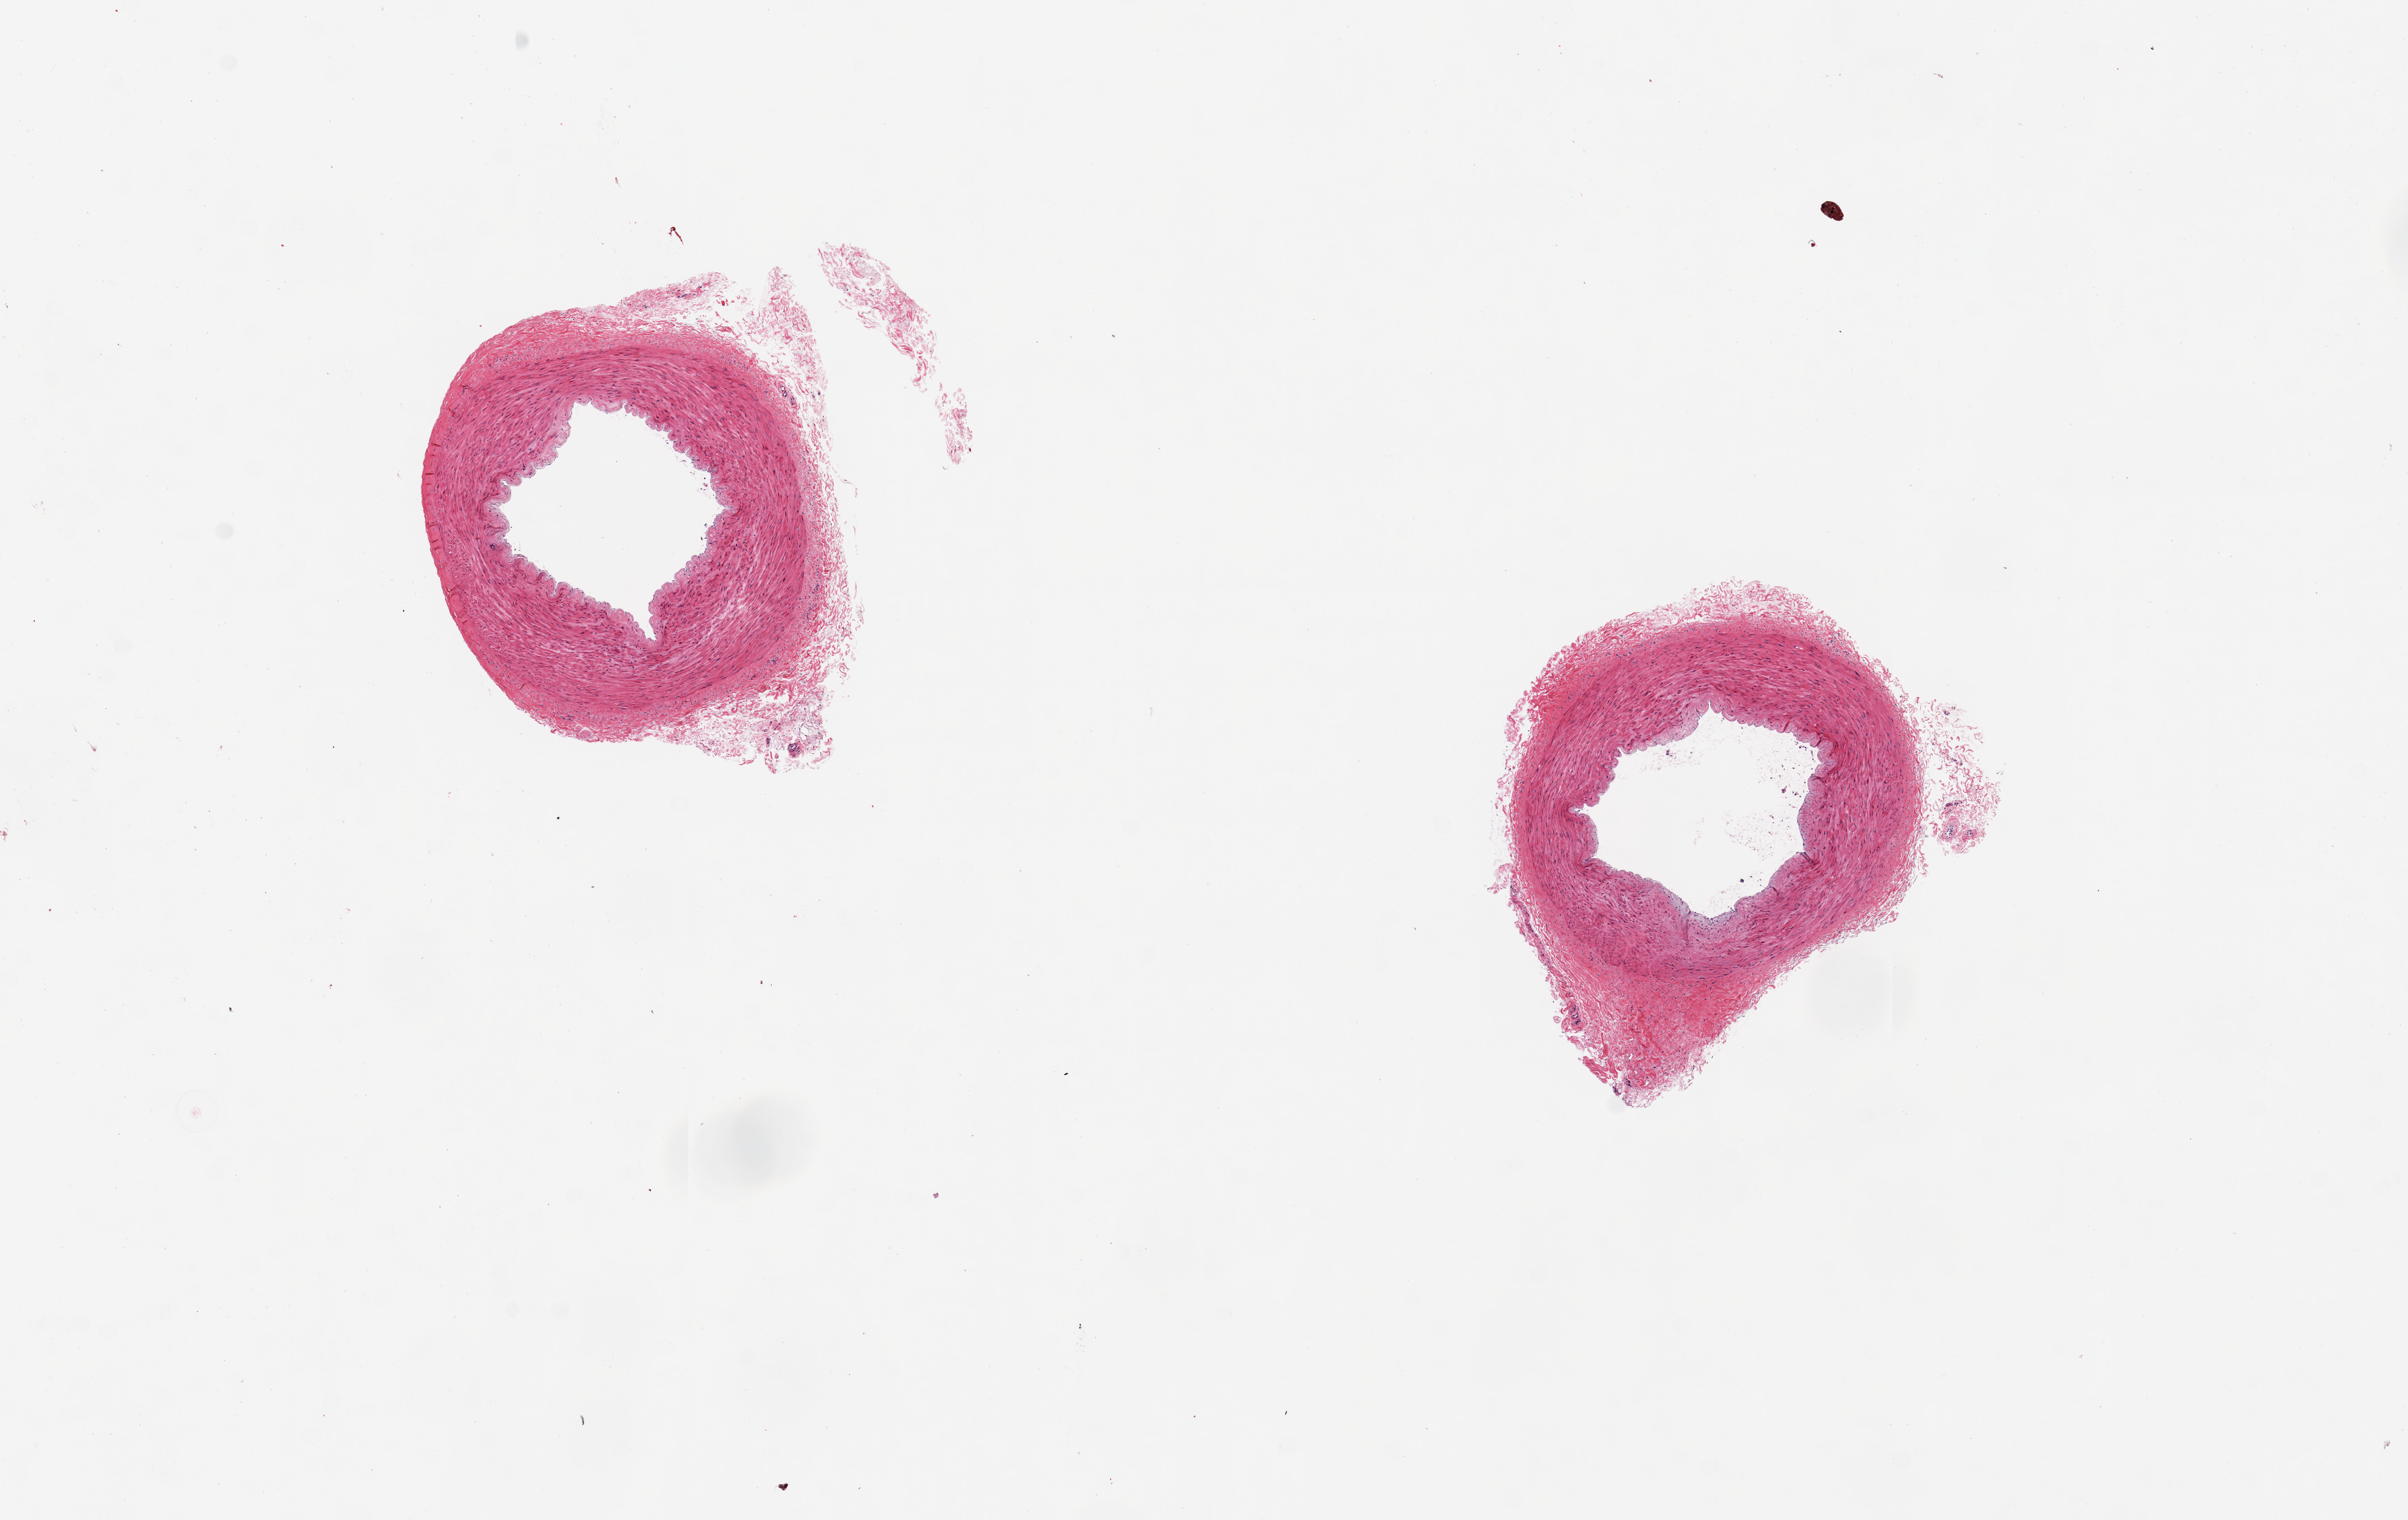
Whole-slide image, hematoxylin and eosin (H&E) stain, whole scanned area (about 13.8 x 8.7 mm) shown as a low-resolution overview; PAXgene-fixed, paraffin-embedded tissue; target tissue: tibial artery; tissue donor sample. Male donor.
- review note (as recorded): 2 pieces, 3x2 & 3x3mm; Well trimmed of extraneous tissue